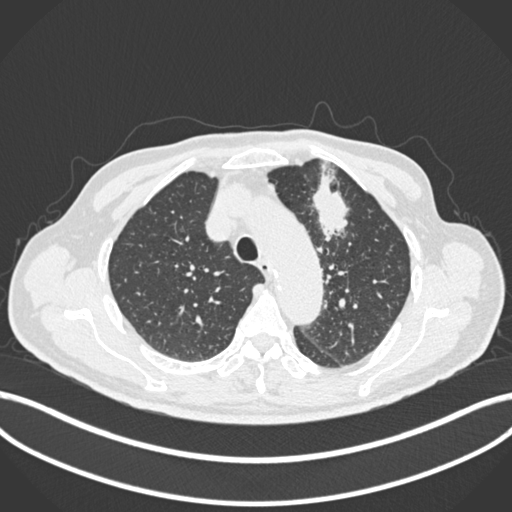
Chest CT, one axial slice. Position 193 of 261 along the scan axis. Lung window (W 1500 / L -600 HU). 512 × 512 image matrix, field of view 400 × 400 mm. Male patient, age 74 years. From the clinical record (not read from this slice): clinical TNM (as recorded): T2b N0 M1c.
Annotated regions visible in this slice (rectangle marked by the reading radiologist):
- lung tumour (recorded histology: adenocarcinoma): bounding box [x1, y1, x2, y2] px = [306, 160, 355, 243]